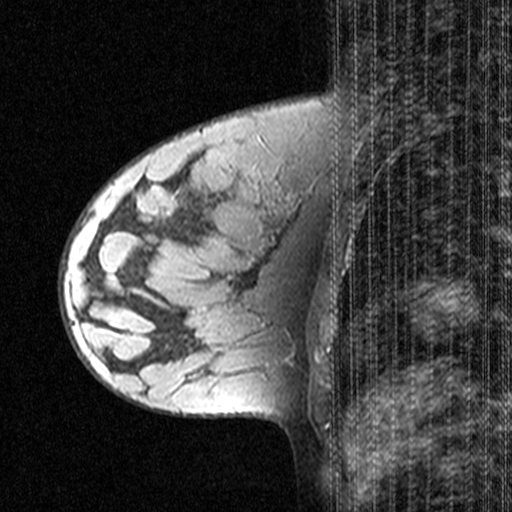
Breast MRI (dynamic contrast-enhanced), one sagittal slice; slice 14 of 44 in the series (ordered by position); dynamic contrast-enhanced study with each time point stored as its own series, time point 2 of 3 at this slice position (early post-contrast, ordered by acquisition time); 1.5 T; TE 4.5 ms, TR 11 ms; 512 × 512 image matrix. Female patient, age 28 years. From the clinical record (not read from this slice): setting: breast cancer imaged before/during neoadjuvant chemotherapy; receptor status: HR-positive, HER2-negative.
Annotated regions visible in this slice (semi-automatically segmented with operator editing):
- analysis volume of interest (the breast-tissue region the enhancement analysis was run in; not a lesion): bounding box (x1, y1, x2, y2) in pixels: (60, 182, 151, 283)
- tumour enhancement mask (voxels above the 90 % enhancement threshold inside the analysis volume of interest): (104, 237, 107, 241)